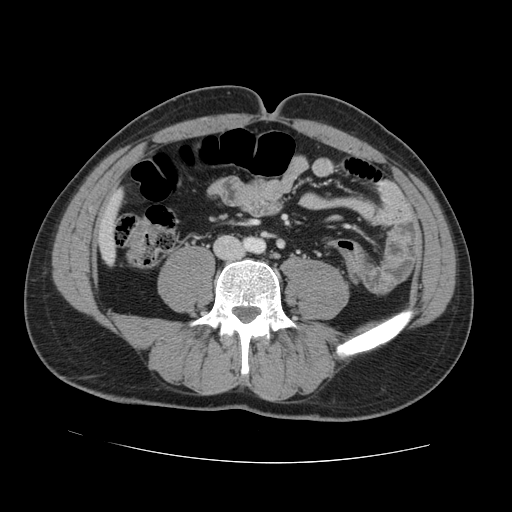
Contrast-enhanced abdominal CT, one axial slice; position 10 of 131 along the scan axis; 120 kVp; intravenous contrast given; soft-tissue window (W 400 / L 40 HU); 2.5 mm slice thickness; 512 × 512 image matrix, field of view 380 × 380 mm. Male patient, age 40 years. Case-level facts recorded for this patient, not image findings: diagnosis: colorectal cancer liver metastases, imaged before liver resection; multiple liver metastases: yes; largest metastasis: 2.9 cm; disease in both lobes: yes.
Outlined on this slice (outlined manually by an expert reader):
- liver: bounding box (x1, y1, x2, y2) in pixels: (100, 196, 120, 261)